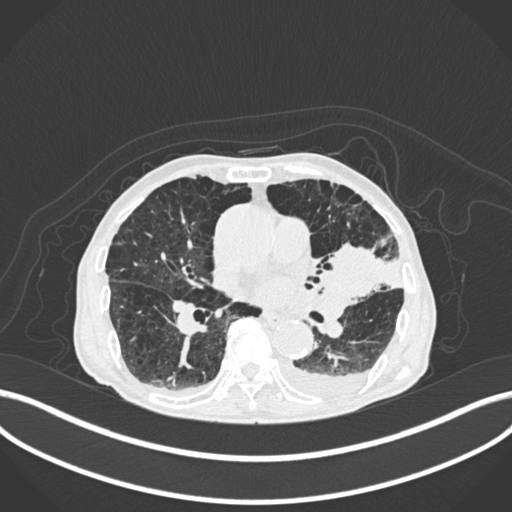
Chest CT, one axial slice. Position 106 of 400 along the scan axis. Reconstruction kernel B30f. Lung window (W 1500 / L -600 HU). 1 mm slice thickness. 512 × 512 image matrix. Patient: male, 90 years or older. From the clinical record (not read from this slice): clinical TNM (as recorded): T2b N1 M0.
Structures marked on this image (rectangle marked by the reading radiologist):
- lung tumour (recorded histology: squamous cell carcinoma): box from (x=317, y=236) to (x=389, y=305) px